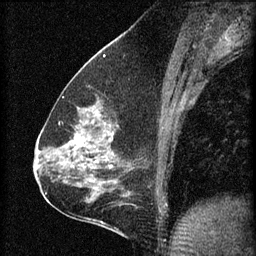
Breast MRI (dynamic contrast-enhanced), one sagittal slice. Slice 34 of 60 in the series (ordered by position). 3 images stored at this slice position (order not interpretable as contrast timing). 1.5 T. TE 4.2 ms, TR 8.2 ms. 2 mm slice thickness. 256 × 256 image matrix. Female patient, age 59 years.
Outlined on this slice (semi-automatically segmented with operator editing):
- analysis volume of interest (the breast-tissue region the enhancement analysis was run in; not a lesion): box from (x=61, y=104) to (x=126, y=161) px
- tumour enhancement mask (voxels above the 70 % enhancement threshold inside the analysis volume of interest): (x=61, y=126)–(x=111, y=161)